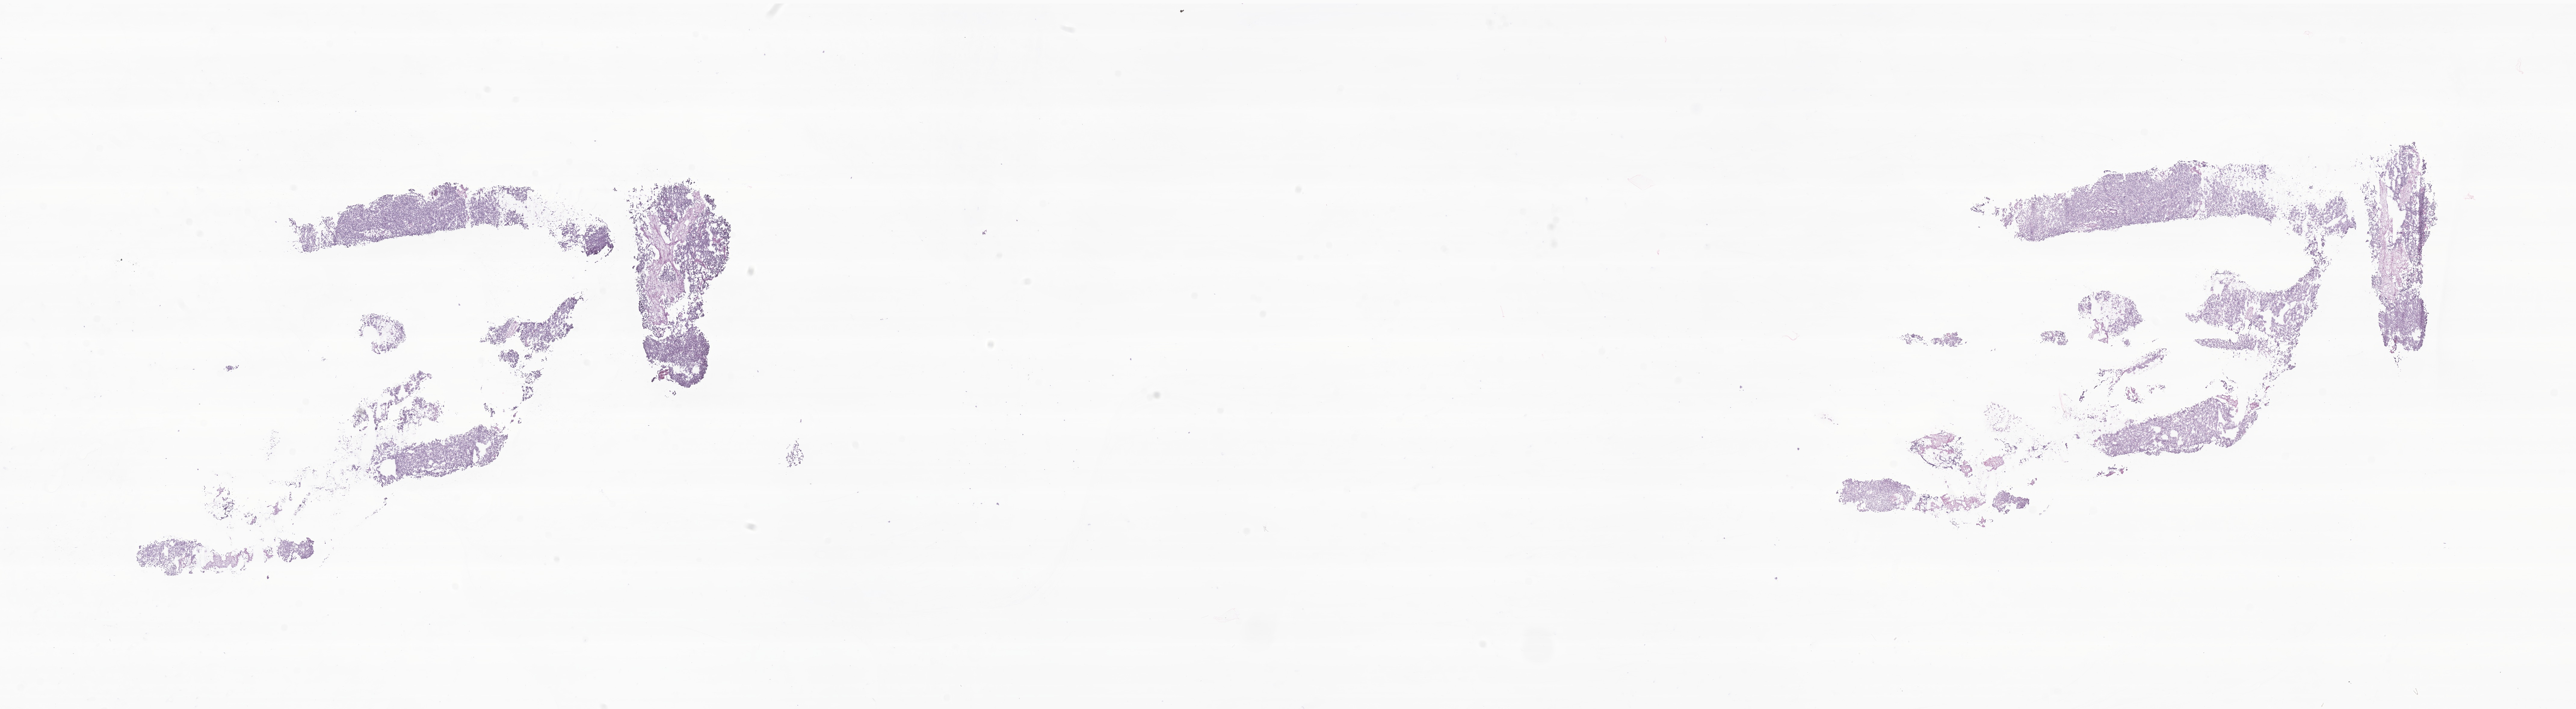
Whole-slide image, hematoxylin and eosin (H&E) stain of tumor tissue from the brain — low-resolution overview of the scanned area, about 36.1 x 9.9 mm; frozen section. Patient: female, age 105 months (8 years 9 months).
- recorded diagnosis: Medulloblastoma, NOS